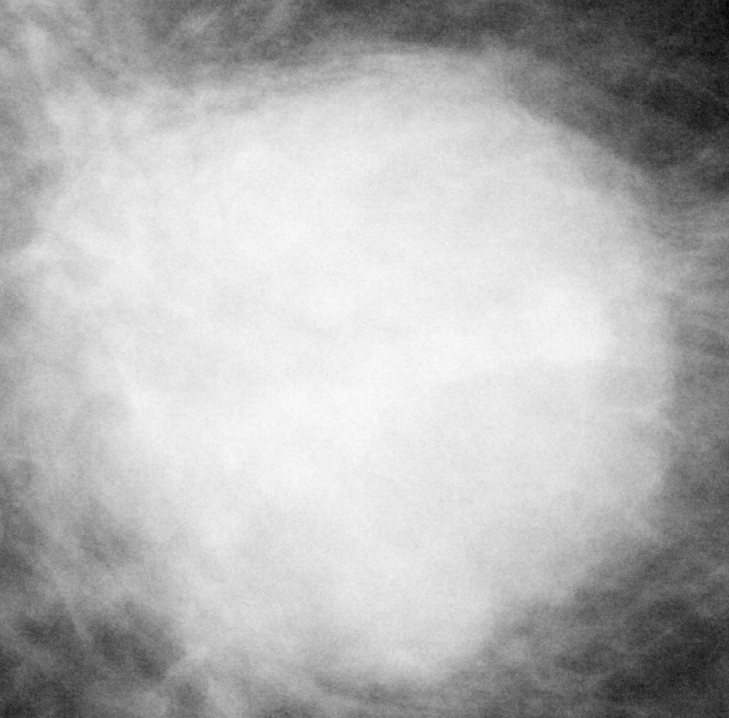
Region of interest cut from a scanned film mammogram (one marked finding); right breast; CC view.
Marked abnormality: mass, shape lobulated, margins microlobulated; BI-RADS assessment category 5; pathology result (as recorded, not read from the image): malignant.